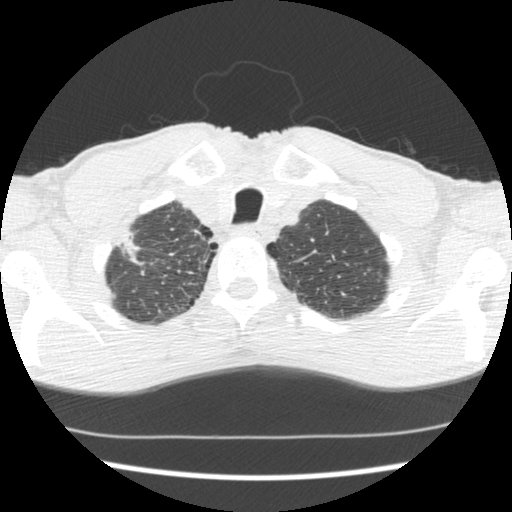
Axial slice from a low-dose chest CT screening exam; baseline screening round; lung window (W 1500 / L -600 HU); 2.5 mm slice thickness; standard (soft-tissue) reconstruction kernel (STANDARD); slice 29 of 197 in the series; 512 × 512 image matrix, field of view 318 × 318 mm. Male, age 62 years at enrolment. Current smoker at enrolment.
Lesion marked by an expert reader, bounding box (x1, y1, x2, y2) in pixels: (100, 226, 150, 274). Screening reader's record for this exam: no non-calcified nodule ≥4 mm recorded. Official screen result: negative screen, significant abnormalities not suspicious for lung cancer. Lung cancer was diagnosed 640 days after this screen (after the second annual screen): adenocarcinoma, NOS, right upper lobe, poorly differentiated (G3), stage IIA (AJCC 6th edition), 22 mm at pathology.